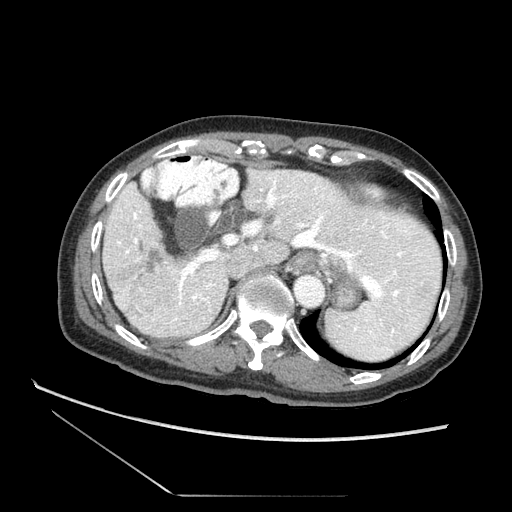
Contrast-enhanced abdominal CT (liver protocol), one axial slice. Position 57 of 73 along the scan axis. 120 kVp. Soft-tissue window (W 400 / L 40 HU). 2.5 mm slice thickness. 512 × 512 image matrix, field of view 360 × 360 mm. From the clinical record (not read from this slice): diagnosis: hepatocellular carcinoma (patient treated with transarterial chemoembolisation; whether this scan precedes or follows treatment is not stated here); TNM stage (as recorded): Stage-II; Child-Pugh class: A; tumour size: 3.8 cm.
Annotated regions visible in this slice (semi-automatically segmented with operator editing):
- liver parenchyma outside the tumour (the mass and vessels are separate outlines, so this box may not span the whole liver): bounding box [x1, y1, x2, y2] px = [104, 169, 445, 355]
- mass: [116, 268, 183, 317]
- liver vessels: [117, 188, 423, 310]